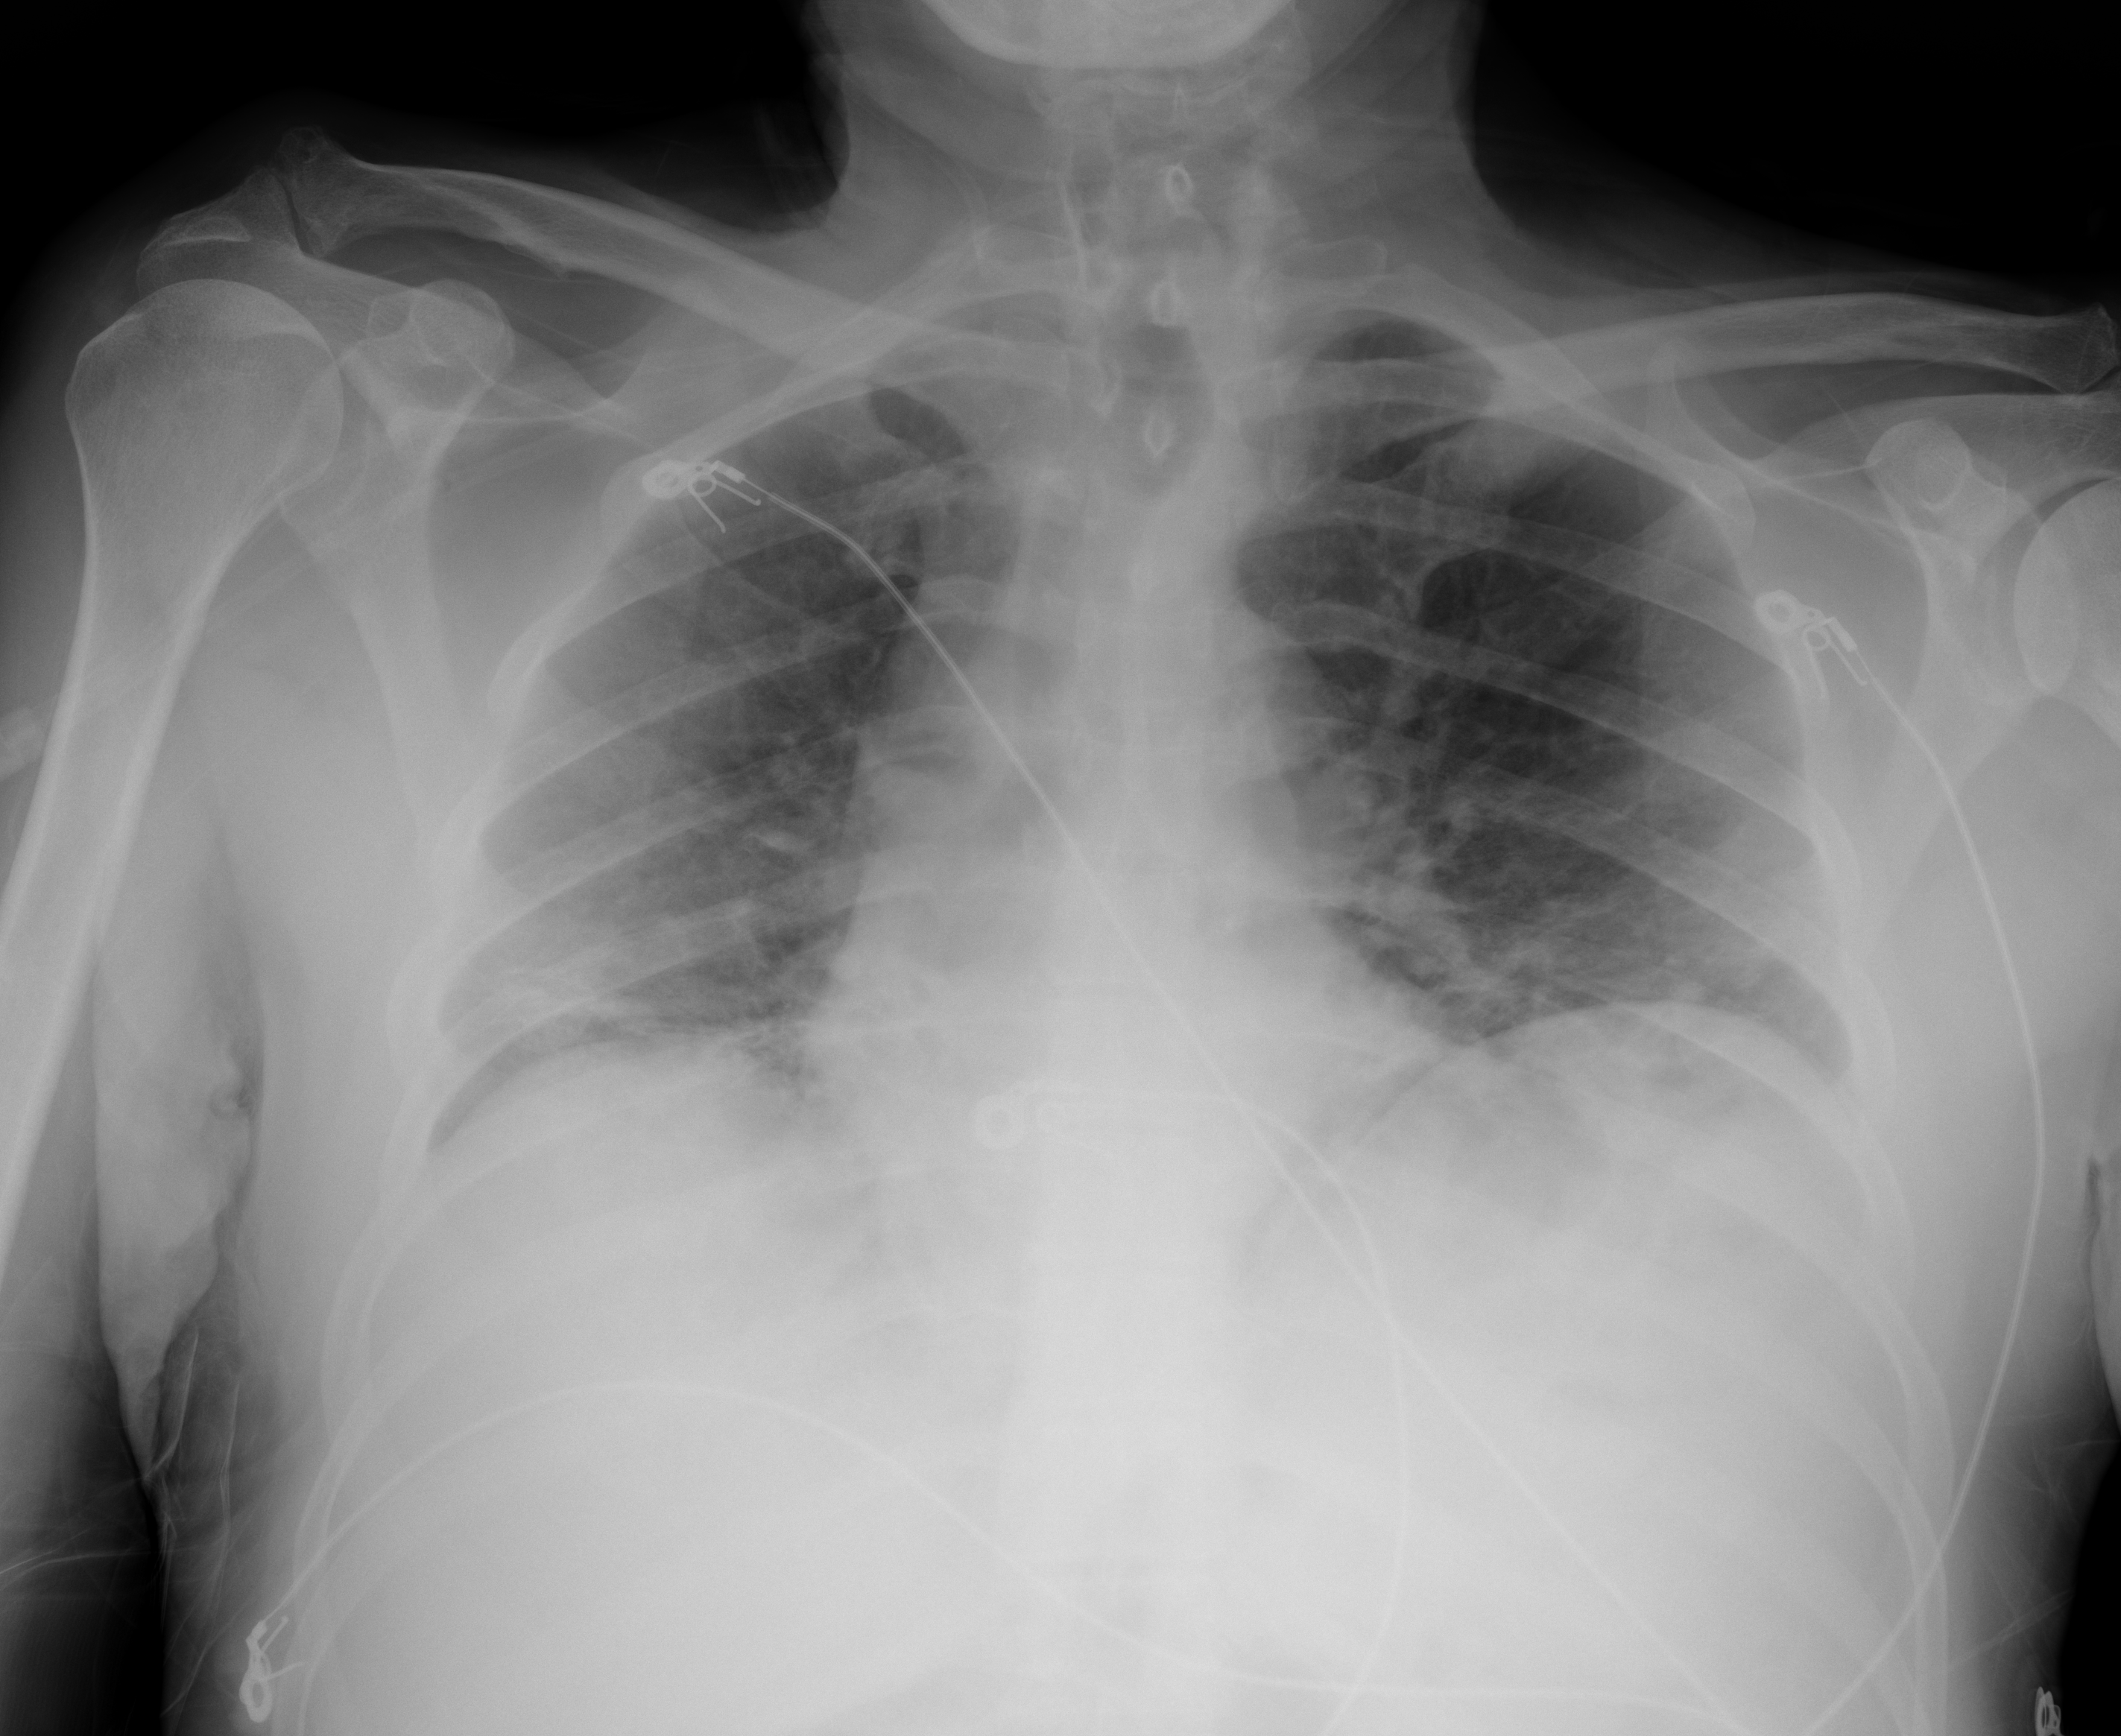
Portable chest radiograph, AP projection. Male patient, age 66 years; imaged 0 days after the COVID-19 diagnosis.
Radiologist key findings (as recorded): Low lung volumes with bibasilar atelectatic changes.